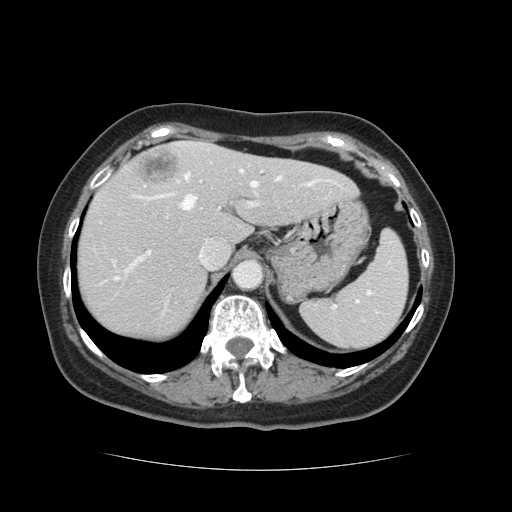
Contrast-enhanced abdominal CT, one axial slice; slice 94 of 128 in the series (ordered by position); 120 kVp; intravenous contrast given; soft-tissue window (W 400 / L 40 HU); 2.5 mm slice thickness; 512 × 512 image matrix, field of view 366 × 366 mm. Female patient, age 67 years. From the clinical record (not read from this slice): diagnosis: colorectal cancer liver metastases, imaged before liver resection; multiple liver metastases: yes; largest metastasis: 3 cm; disease in both lobes: yes.
Annotated regions visible in this slice (expert manual segmentation):
- hepatic veins: bounding box (x1, y1, x2, y2) in pixels: (116, 170, 282, 279)
- liver: (77, 143, 354, 339)
- planned liver remnant (the part of the liver to remain after resection): (76, 157, 354, 339)
- portal vein (with intrahepatic branches): (132, 160, 263, 268)
- liver metastasis: (135, 150, 179, 185)